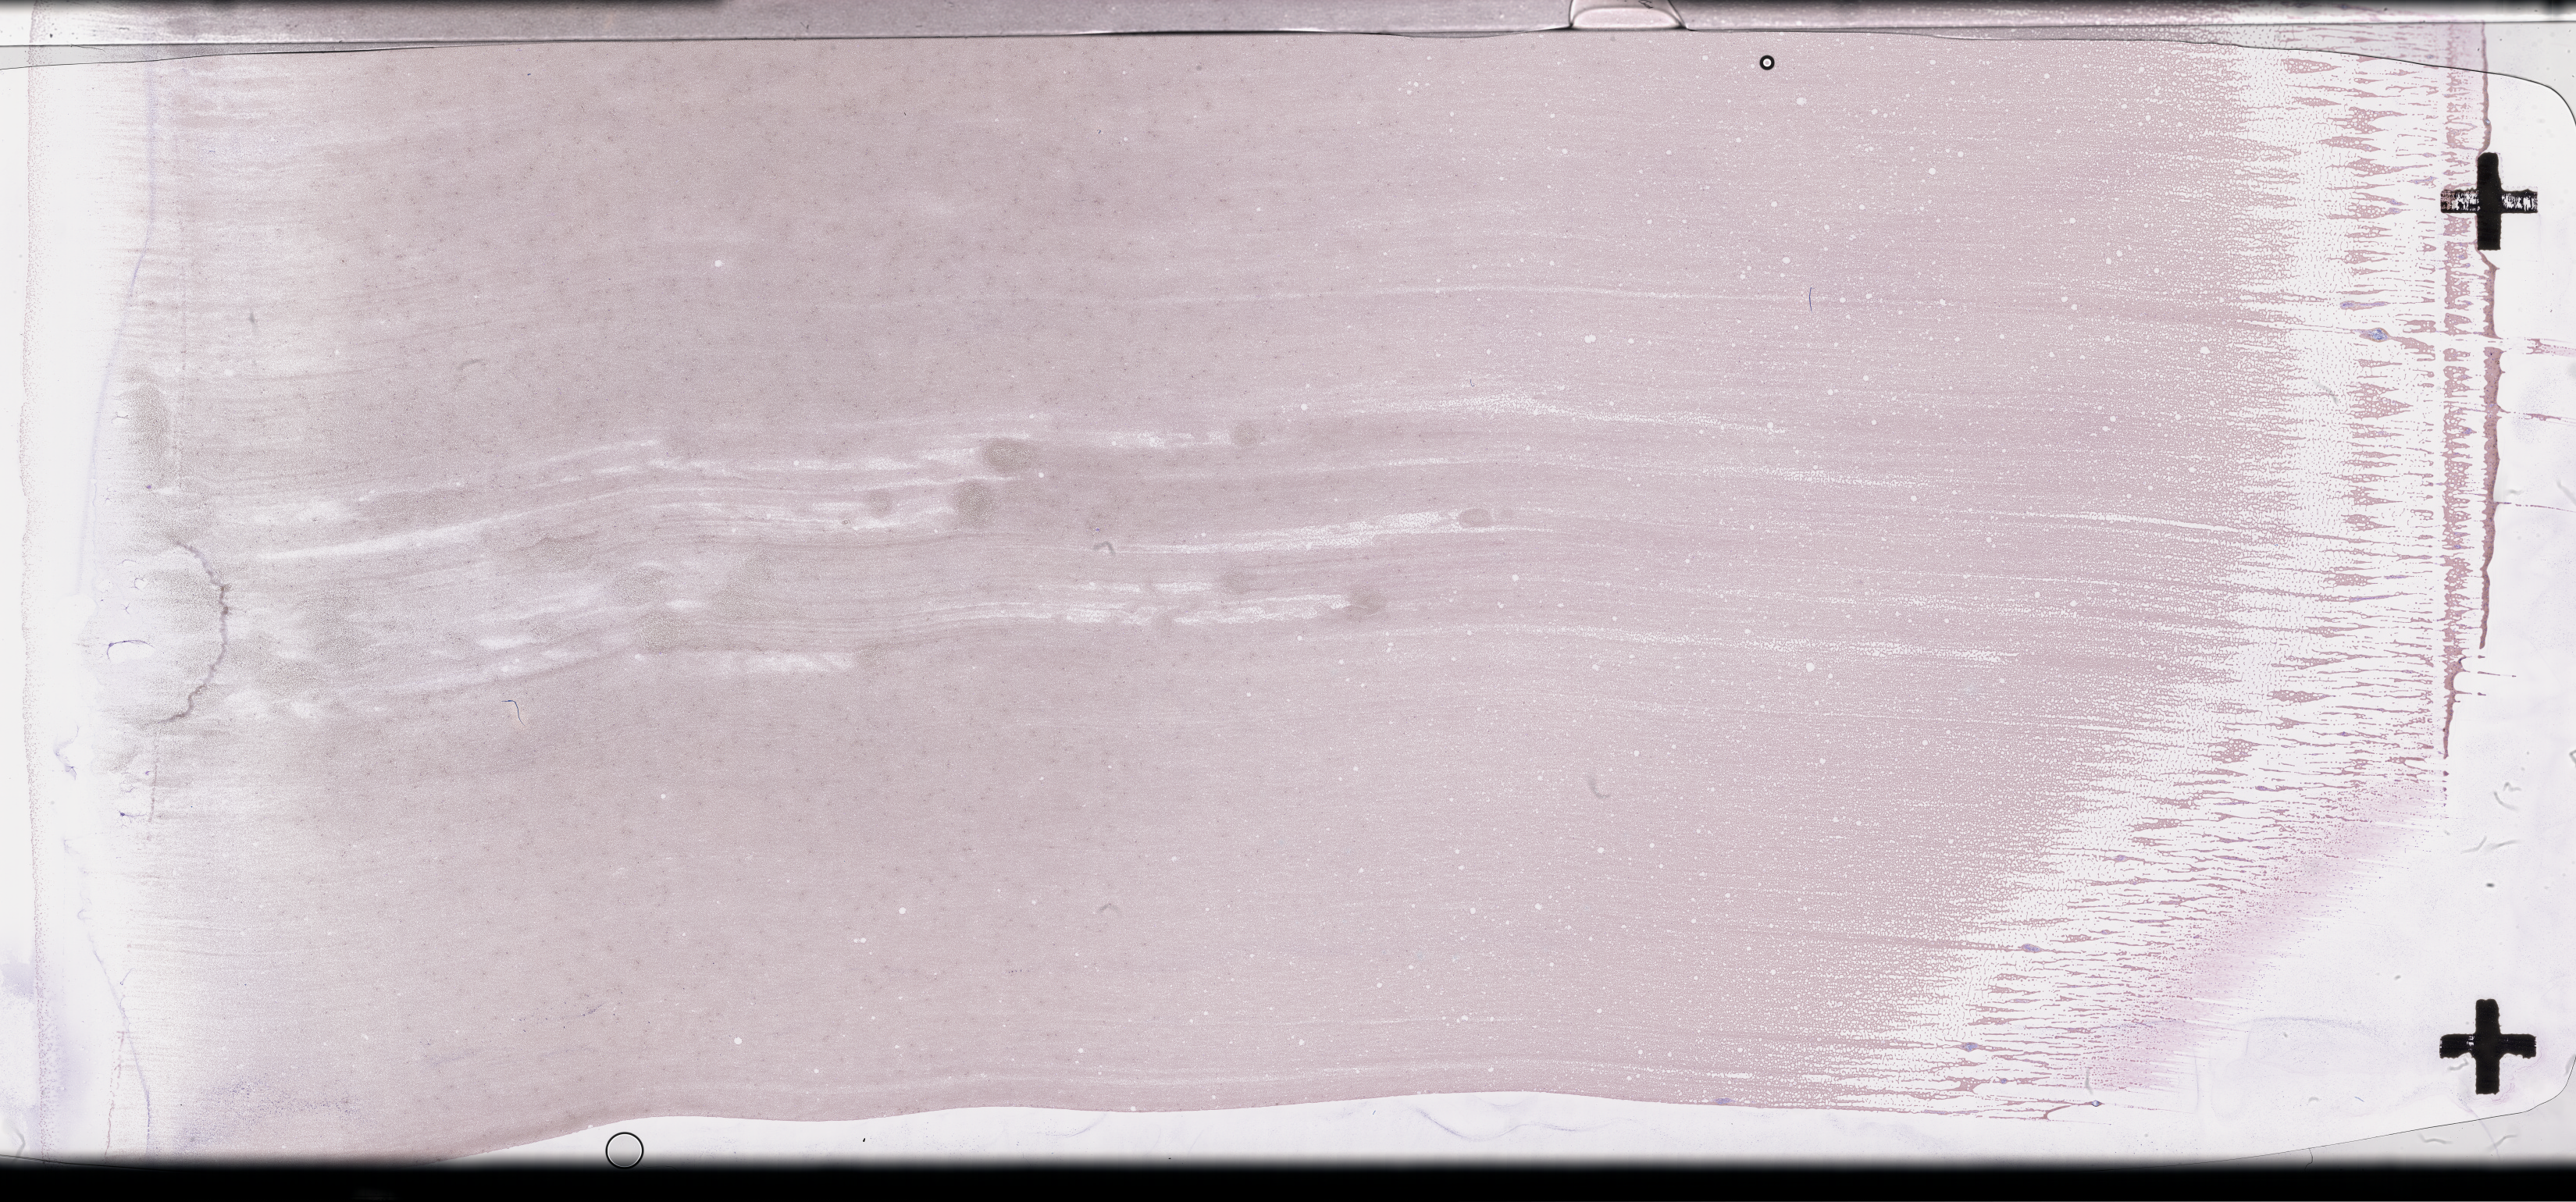
Wright–Giemsa-stained whole blood smear, whole-slide image, shown as a low-resolution overview of the whole scanned area (about 53.3 x 24.9 mm); specimen time point: collected on treatment. Patient: male.
- from a patient with: Plasma Cell Myeloma